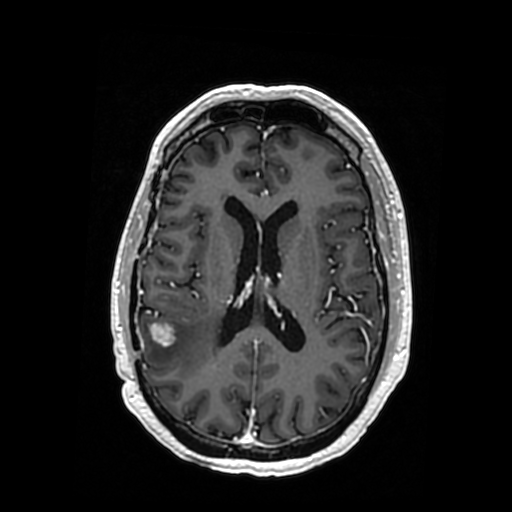
Brain MRI from a brain-tumour surgery series, one axial slice. Slice 159 of 364 in the series (ordered by position). T1-weighted post-contrast. 0.5 mm slice thickness. 512 × 512 image matrix. Case-level facts recorded for this patient, not image findings: histopathology: Oligodendroglioma; WHO grade: 3; IDH mutation: yes.
Outlined on this slice (outlined manually by an expert reader):
- tumour: box from (x=146, y=322) to (x=217, y=370) px